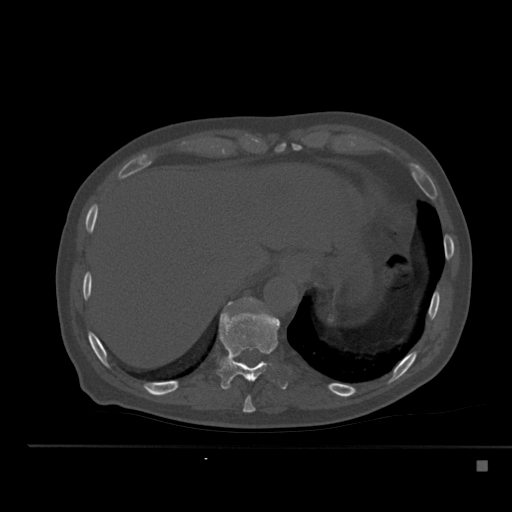
CT including the spine, one axial slice. Slice 268 of 517 in the series (ordered by position). 120 kVp. Bone window (W 1800 / L 400 HU). 1.5 mm slice thickness. 512 × 512 image matrix, field of view 408 × 408 mm. Patient: male, 70 years. From the clinical record (not read from this slice): primary cancer: renal; vertebrae with lytic lesions (as recorded): T4, T6, T10, T12, L3, L4, L5.
Structures marked on this image (semi-automatic segmentation, software-assisted and operator-edited):
- T10 vertebra: bounding box <217,309,280,389> (left, top, right, bottom; pixels)
- T11 vertebra: <227,297,263,306>
- T9 vertebra: <243,396,255,413>